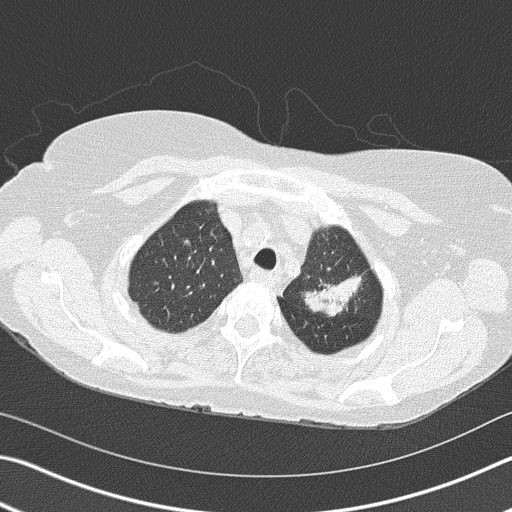
Axial slice from a low-dose chest CT screening exam; second screening round (one year after baseline); lung window (W 1500 / L -600 HU); 120 kVp; slice 130 of 153 in the series. Female, age 68 years at enrolment. Former smoker at enrolment.
Lesion marked by an expert reader, box from (x=290, y=236) to (x=374, y=326) px. Screening reader's record for this exam (one nodule recorded; not confirmed to be the boxed lesion): non-calcified nodule or mass ≥4 mm, left upper lobe, 4 × 2 mm, spiculated (stellate) margins, soft tissue attenuation, pre-existing on the prior screen: yes; interval growth: yes. Official screen result: positive, other. Lung cancer was diagnosed 392 days after this screen: adenocarcinoma, NOS, left upper lobe, poorly differentiated (G3), stage IB (AJCC 6th edition), 50 mm at pathology.